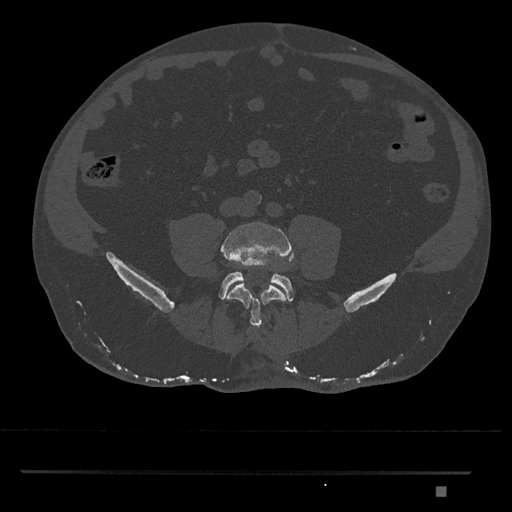
CT including the spine, one axial slice; position 588 of 1134 along the scan axis; reconstruction kernel Br40s/3; 120 kVp; bone window (W 1800 / L 400 HU); 0.5 mm slice thickness; 512 × 512 image matrix, field of view 429 × 429 mm. Patient: male, 65 years. From the clinical record (not read from this slice): primary cancer: prostate.
Outlined on this slice (semi-automatically segmented with operator editing):
- L4 vertebra: box from (x=220, y=222) to (x=294, y=328) px
- L5 vertebra: (x=218, y=272)–(x=294, y=301)